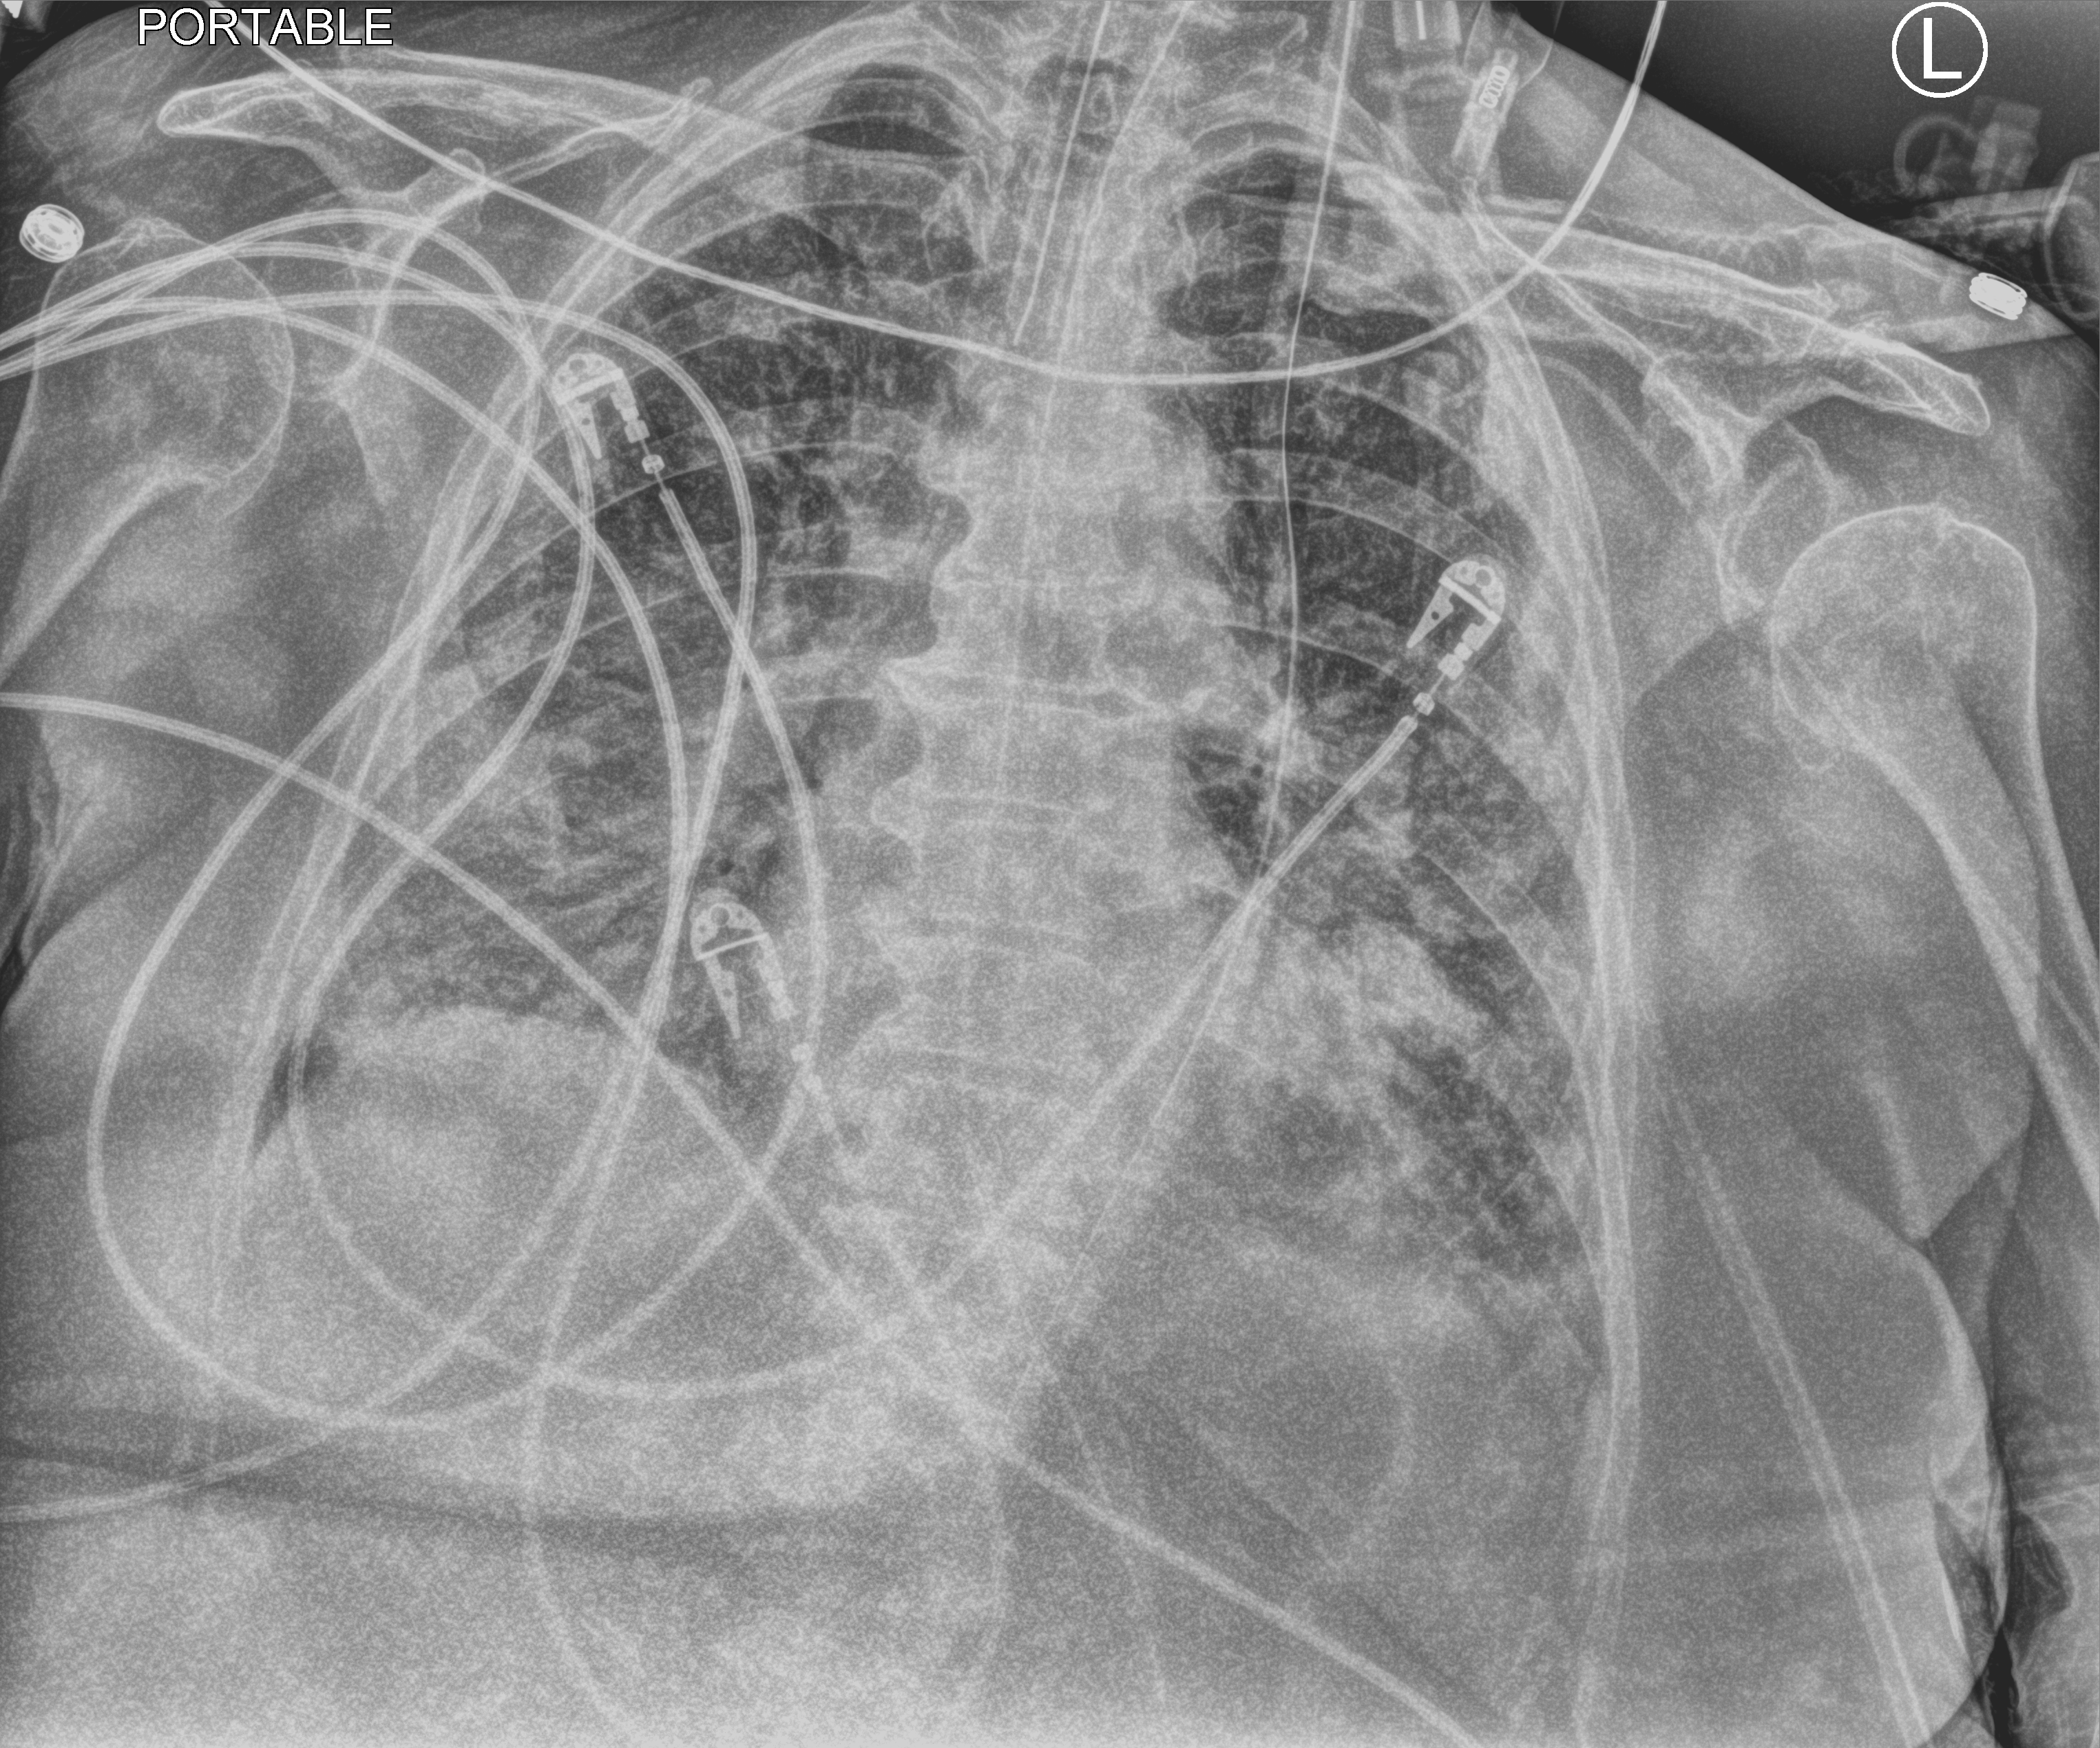
Bedside chest radiograph (computed radiography); anteroposterior (AP) projection. Female patient hospitalised with COVID-19, age 75–90 years.
Admission-level facts for this patient (not findings on this image; timing relative to this image not recorded):
- diabetes (admission record): no
- admitted to intensive care during this hospital stay: no